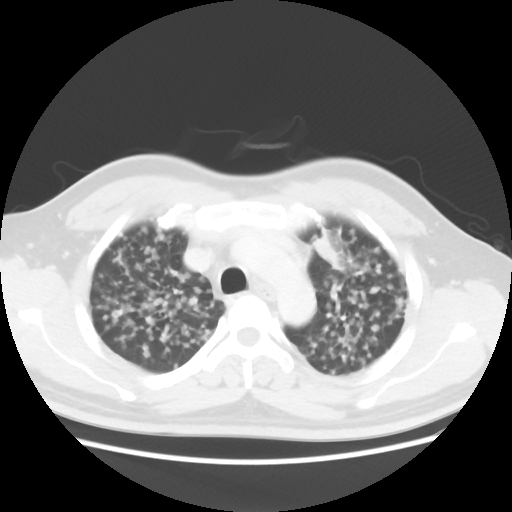
Chest CT, one axial slice. Position 30 of 40 along the scan axis. Reconstruction kernel STANDARD. 120 kVp. Lung window (W 1500 / L -600 HU). 512 × 512 image matrix, field of view 366 × 366 mm. Patient: male, 41 years. From the clinical record (not read from this slice): clinical TNM (as recorded): T1c N3 M1b; histopathological grade: G2-3.
Outlined on this slice (rectangle marked by the reading radiologist):
- lung tumour (recorded histology: adenocarcinoma): bounding box <313,221,345,278> (left, top, right, bottom; pixels)